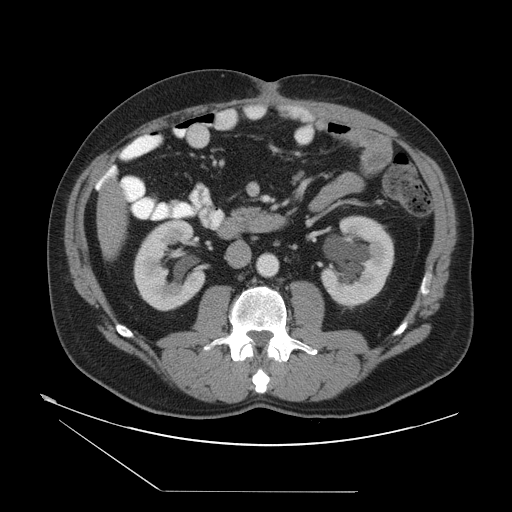
Contrast-enhanced abdominal CT, one axial slice. Slice 14 of 55 in the series (ordered by position). Reconstruction kernel STANDARD. 120 kVp. Intravenous contrast given. Soft-tissue window (W 400 / L 40 HU). 512 × 512 image matrix, field of view 454 × 454 mm. Male patient, age 59 years. Case-level facts recorded for this patient, not image findings: diagnosis: colorectal cancer liver metastases, imaged before liver resection; multiple liver metastases: yes; largest metastasis: 0.3 cm; chemotherapy before resection: yes.
Outlined on this slice (outlined manually by an expert reader):
- liver: box from (x=98, y=186) to (x=126, y=252) px
- planned liver remnant (the part of the liver to remain after resection): (x=98, y=186)–(x=125, y=251)